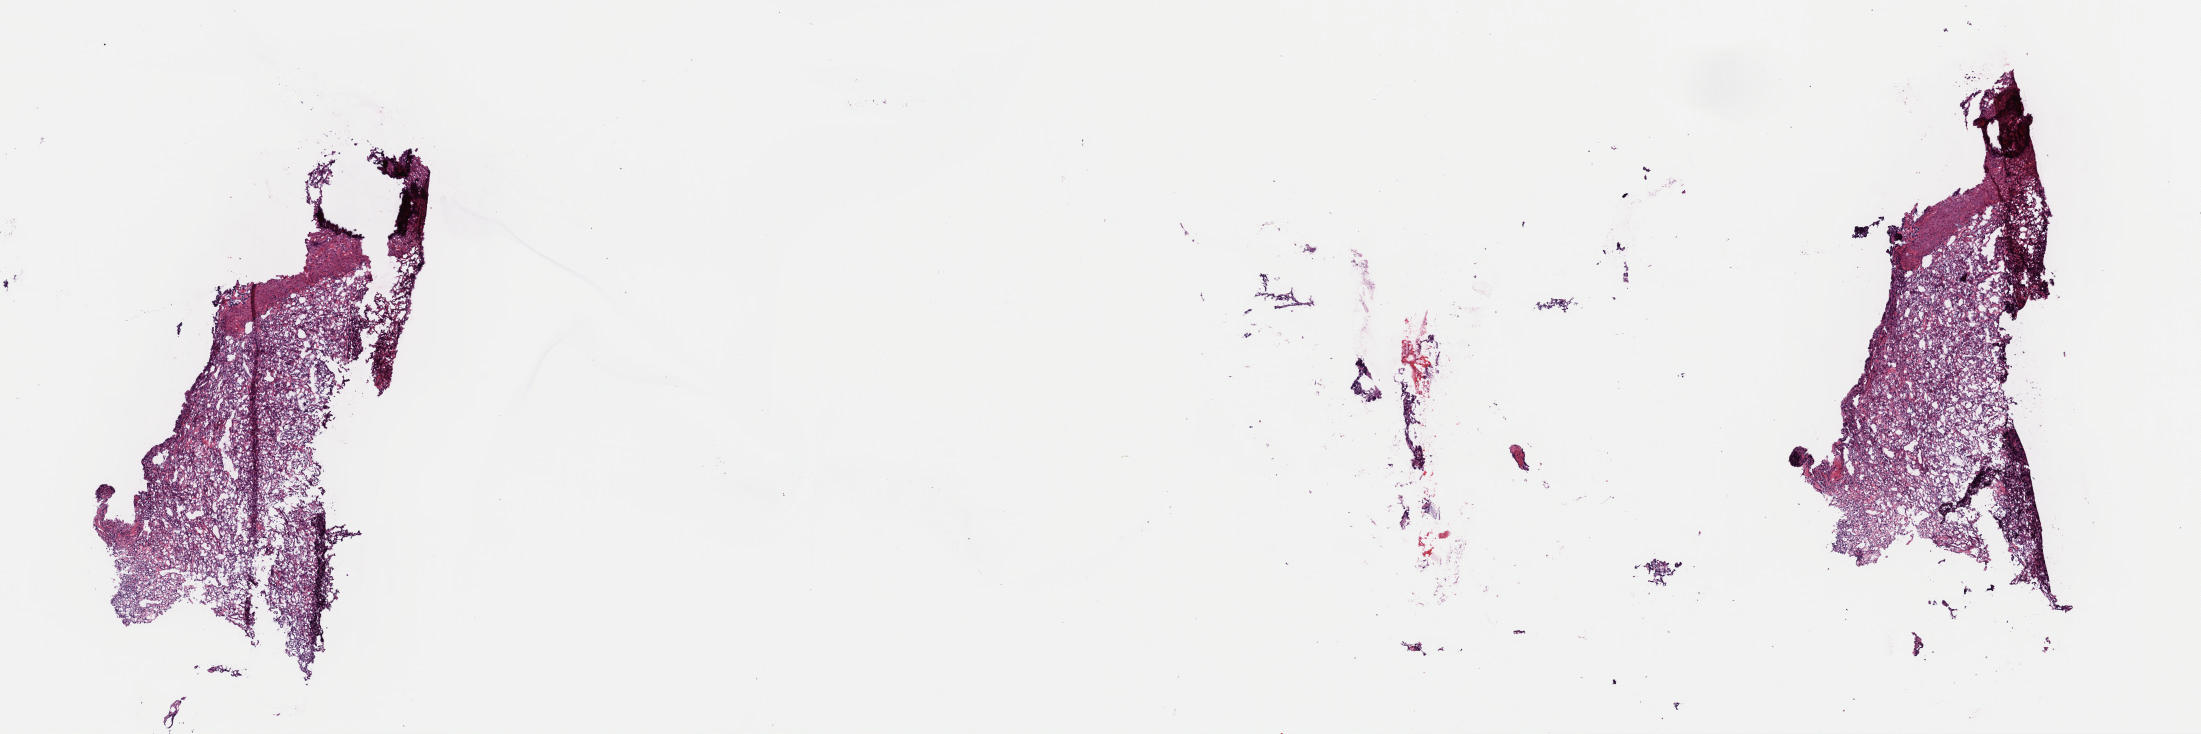
Whole-slide histology image, Hematoxylin and eosin (H&E) stained, shown as a low-resolution overview of the whole scanned area (about 17.4 x 5.8 mm, acquisition: 40x scan). Frozen section. Primary tumour sample from the adrenal gland. Female patient; age at initial diagnosis 42 years. Slide review estimates, as recorded: tumour cells 80%, tumour nuclei 100%, normal cells 0%, stromal cells 20%, necrosis 0%. Infiltration values recorded for this section: lymphocyte infiltration 0%, monocyte infiltration 0%, neutrophil infiltration 0%.
Histologic diagnosis: Pheochromocytoma, NOS. Laterality: right.